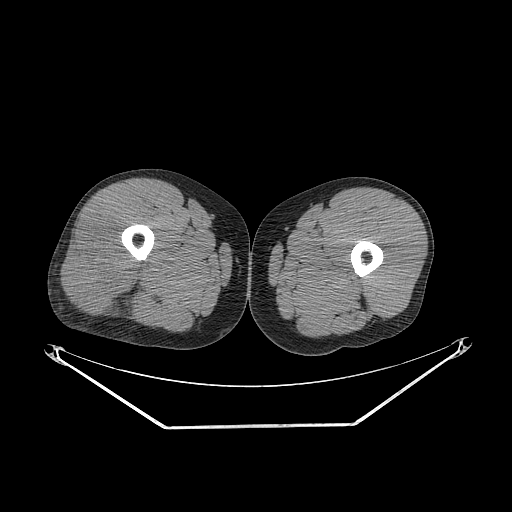
CT of an extremity soft-tissue mass (from a PET/CT study), one axial slice; position 248 of 267 along the scan axis; 140 kVp; soft-tissue window (W 400 / L 40 HU); 3.75 mm slice thickness; 512 × 512 image matrix, field of view 500 × 500 mm. Male patient. Case-level facts recorded for this patient, not image findings: histological type: poorly differentiated synovial sarcoma; grade: high; site of the primary tumour: right buttock.
Structures marked on this image (expert contour drawn on MRI and transferred to this co-registered scan by the dataset authors):
- gross tumour volume including surrounding oedema: box from (x=60, y=221) to (x=140, y=314) px
- gross tumour volume (mass): (x=60, y=221)–(x=138, y=314)